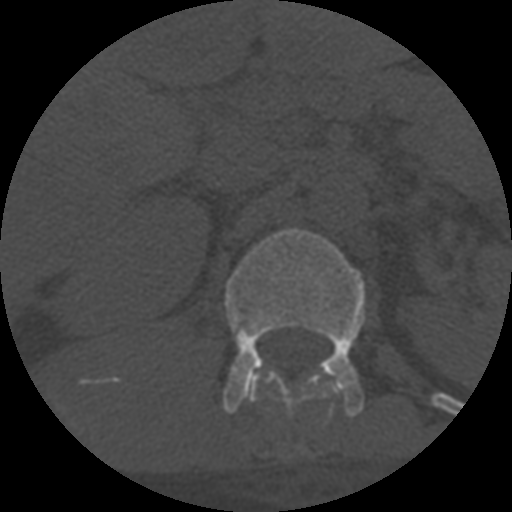
CT including the spine, one axial slice. Slice 296 of 708 in the series (ordered by position). 120 kVp. One of 3 acquisitions stored at this slice position. Bone window (W 1800 / L 400 HU). 1.25 mm slice thickness. 512 × 512 image matrix. Patient age 55 years. From the clinical record (not read from this slice): primary cancer: colon; vertebrae with lytic lesions (as recorded): T12, L1, L5.
Structures marked on this image (semi-automatically segmented with operator editing):
- L1 vertebra: bounding box [x1, y1, x2, y2] px = [222, 229, 366, 417]
- T12 vertebra: [248, 372, 328, 417]